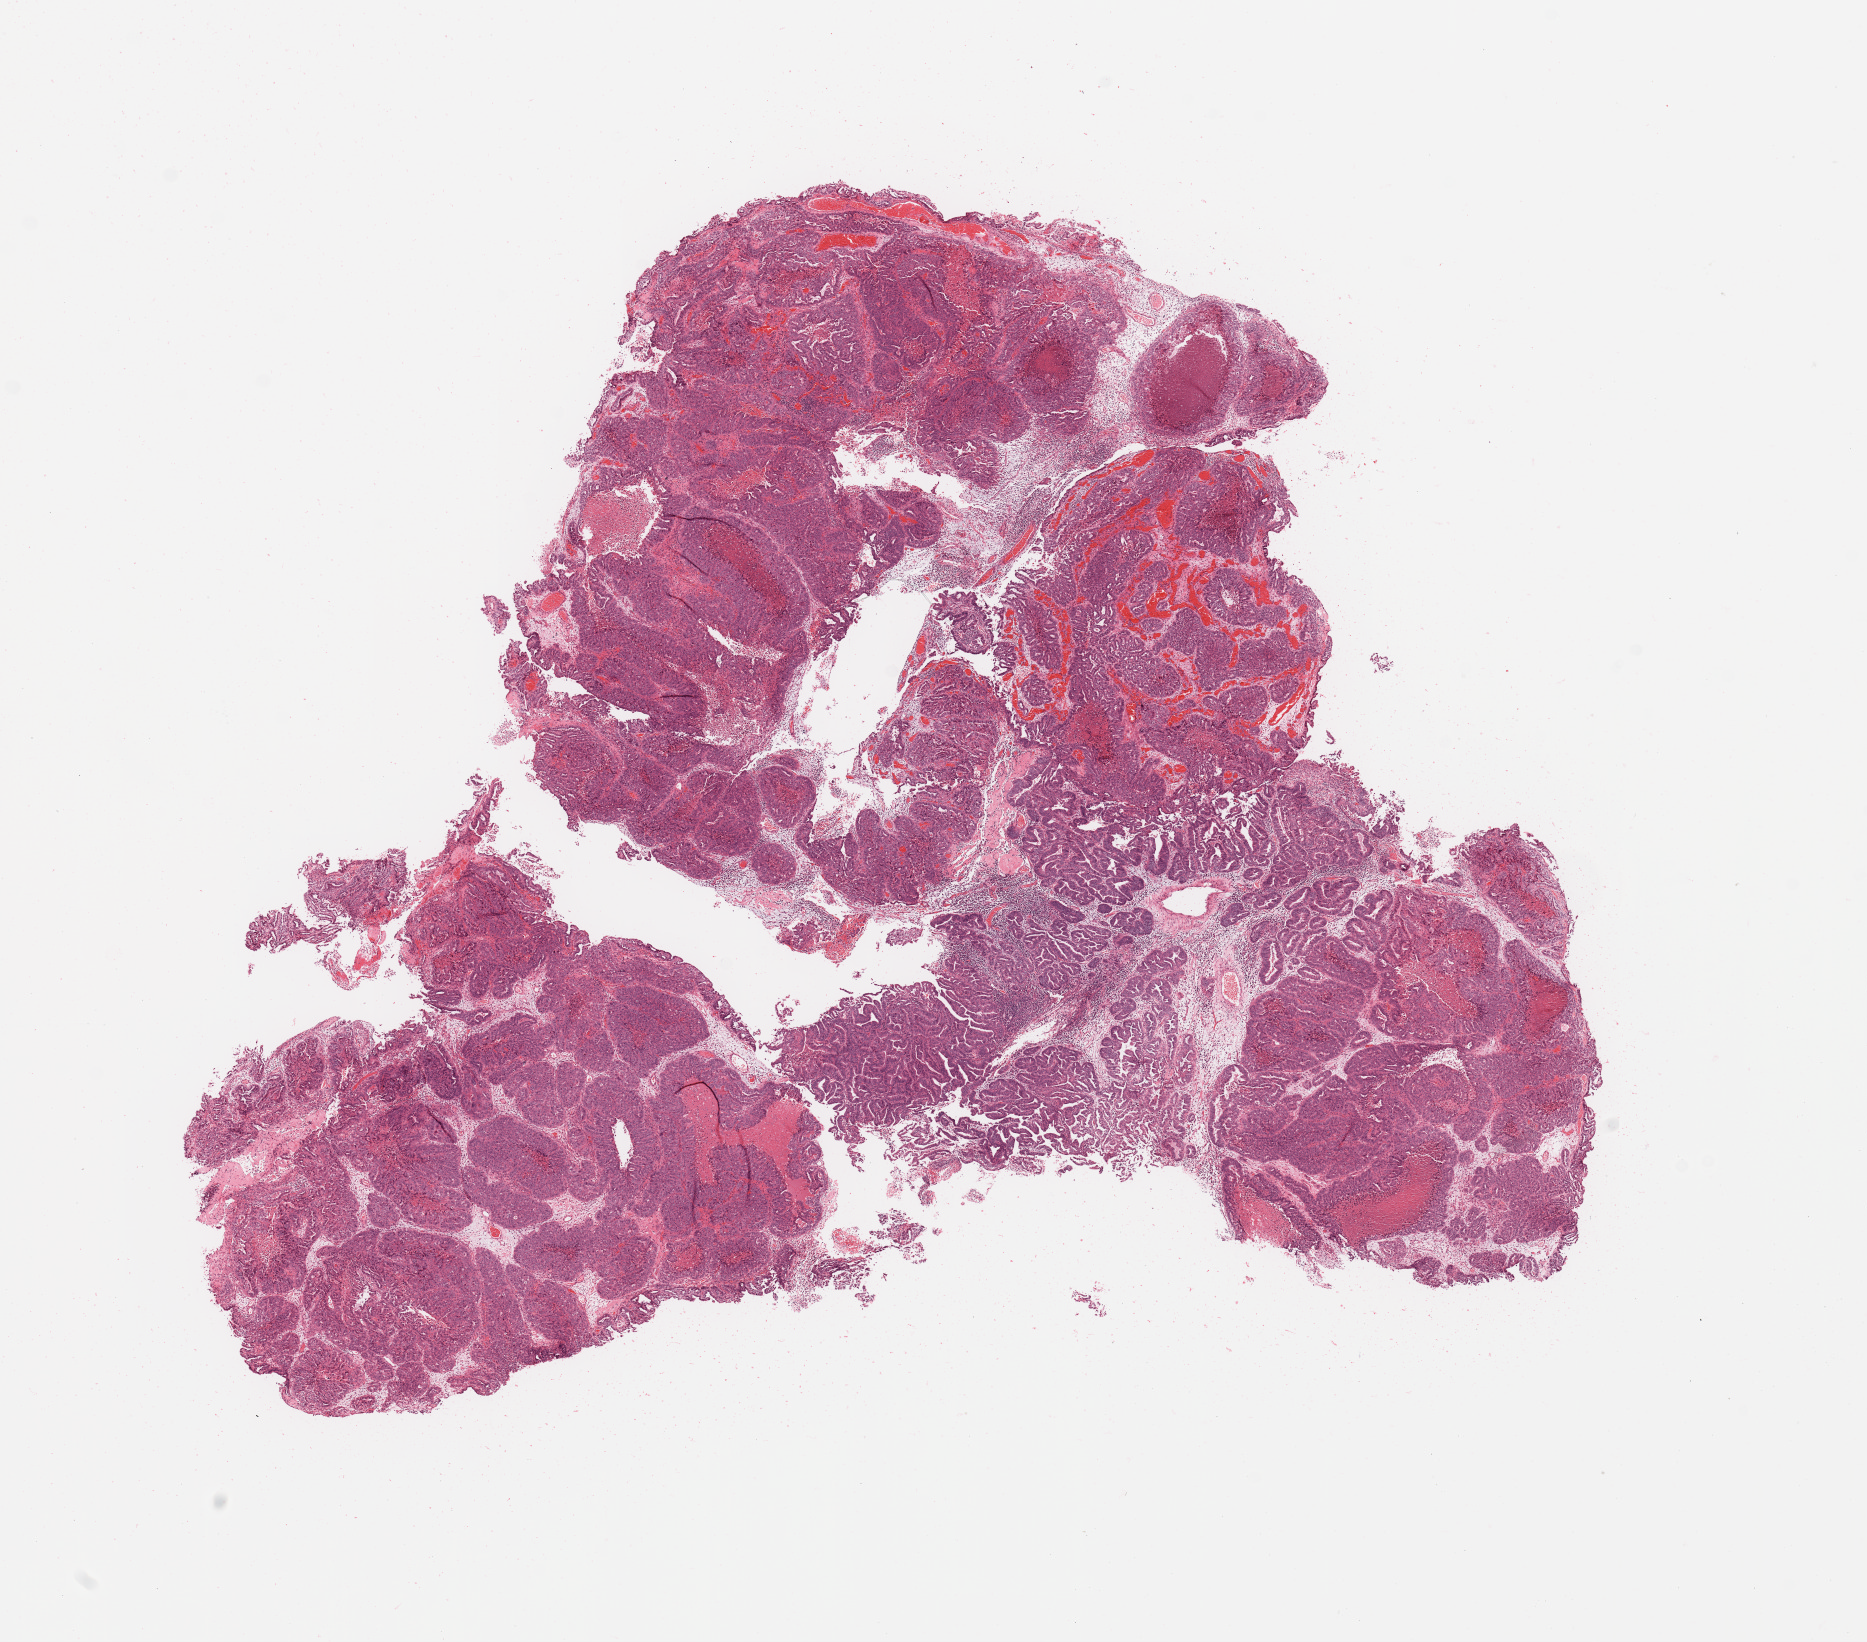
Whole-slide histology image, H&E-stained — shown as a low-resolution overview of the whole scanned area (about 14.8 x 13.0 mm, acquisition: 20x scan); uterus, tumour tissue. 81-year-old female patient. Histologic grade: G2 (moderately differentiated).
Diagnosis: Endometrioid adenocarcinoma, NOS. AJCC pathologic stage: I.